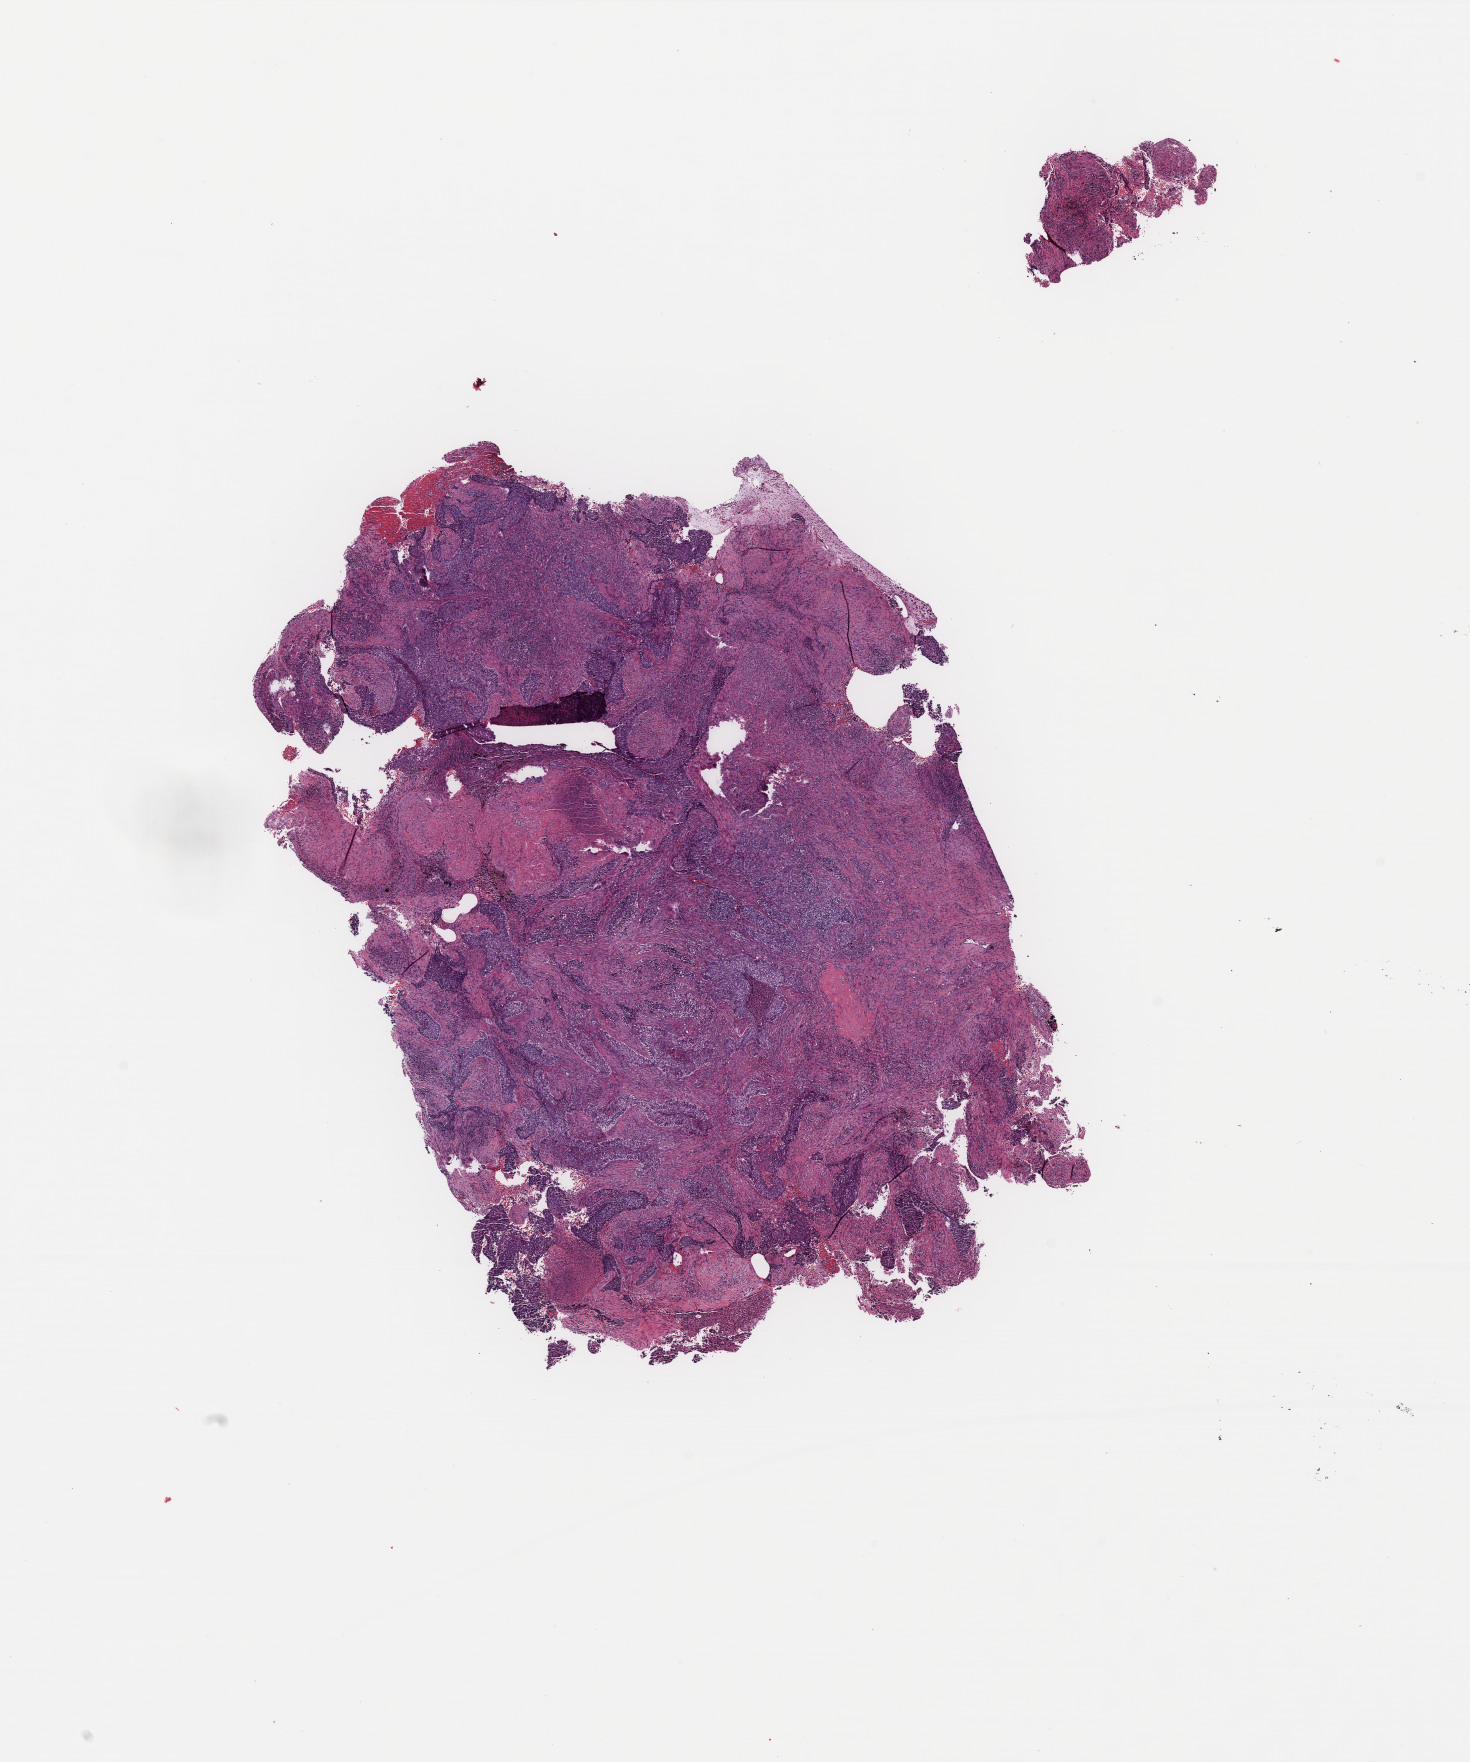
Digitized H&E-stained tissue section (whole slide), shown as a low-resolution overview of the whole scanned area (about 11.8 x 14.1 mm, acquisition: 40x scan); FFPE section; primary tumour sample from the lung. Female patient; age at initial diagnosis 72 years.
Diagnosis: Squamous cell carcinoma, NOS.